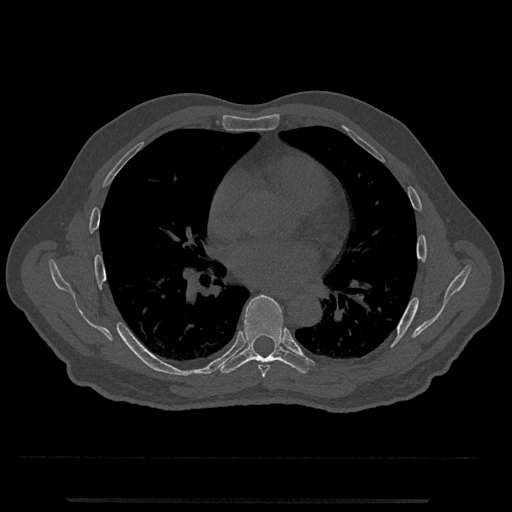
CT including the spine, one axial slice; slice 702 of 797 in the series (ordered by position); reconstruction kernel Br40s/3; 120 kVp; bone window (W 1800 / L 400 HU); 0.5 mm slice thickness; 512 × 512 image matrix, field of view 419 × 419 mm. Male patient, age 63 years. From the clinical record (not read from this slice): primary cancer: prostate.
Annotated regions visible in this slice (semi-automatic segmentation, software-assisted and operator-edited):
- T6 vertebra: bounding box <258,365,270,378> (left, top, right, bottom; pixels)
- T7 vertebra: <218,295,312,374>